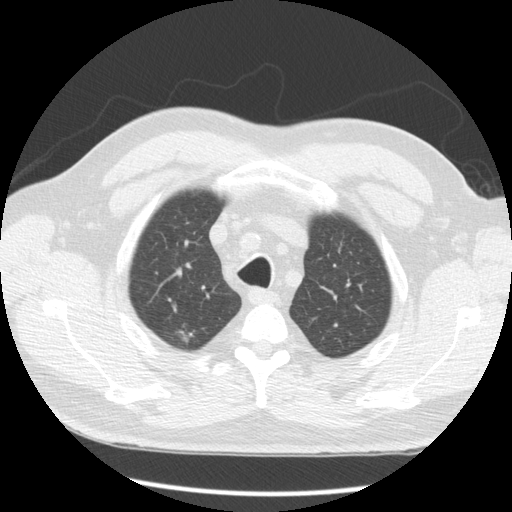
Low-dose screening chest CT, one axial slice. Slice 142 of 163 in the series (ordered by position). Reconstruction kernel STANDARD. 120 kVp. Lung window (W 1500 / L -600 HU). 2.5 mm slice thickness. 512 × 512 image matrix, field of view 360 × 360 mm.
Structures marked on this image (outlined manually by an expert reader):
- lesion 1 (tumor, upper lobe of right lung): bounding box (x1, y1, x2, y2) in pixels: (178, 331, 192, 343)